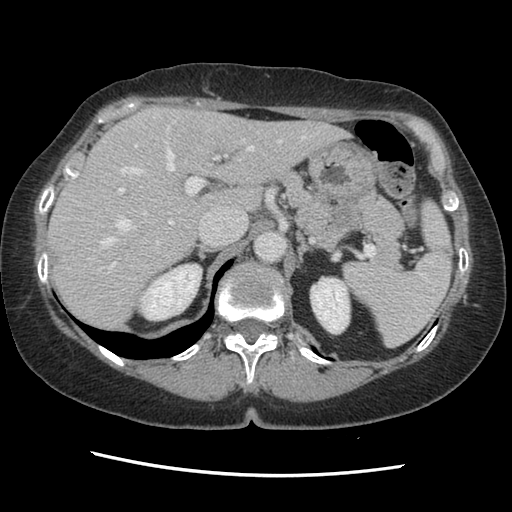
Contrast-enhanced abdominal CT, one axial slice. Slice 93 of 141 in the series (ordered by position). 120 kVp. Soft-tissue window (W 400 / L 40 HU). 512 × 512 image matrix. Female patient, age 61 years. From the clinical record (not read from this slice): diagnosis: colorectal cancer liver metastases, imaged before liver resection; multiple liver metastases: no; largest metastasis: 2.4 cm; disease in both lobes: no.
Outlined on this slice (expert manual segmentation):
- hepatic veins: bounding box <101,121,306,247> (left, top, right, bottom; pixels)
- liver: <49,108,344,332>
- planned liver remnant (the part of the liver to remain after resection): <49,108,344,332>
- portal vein (with intrahepatic branches): <99,144,227,271>